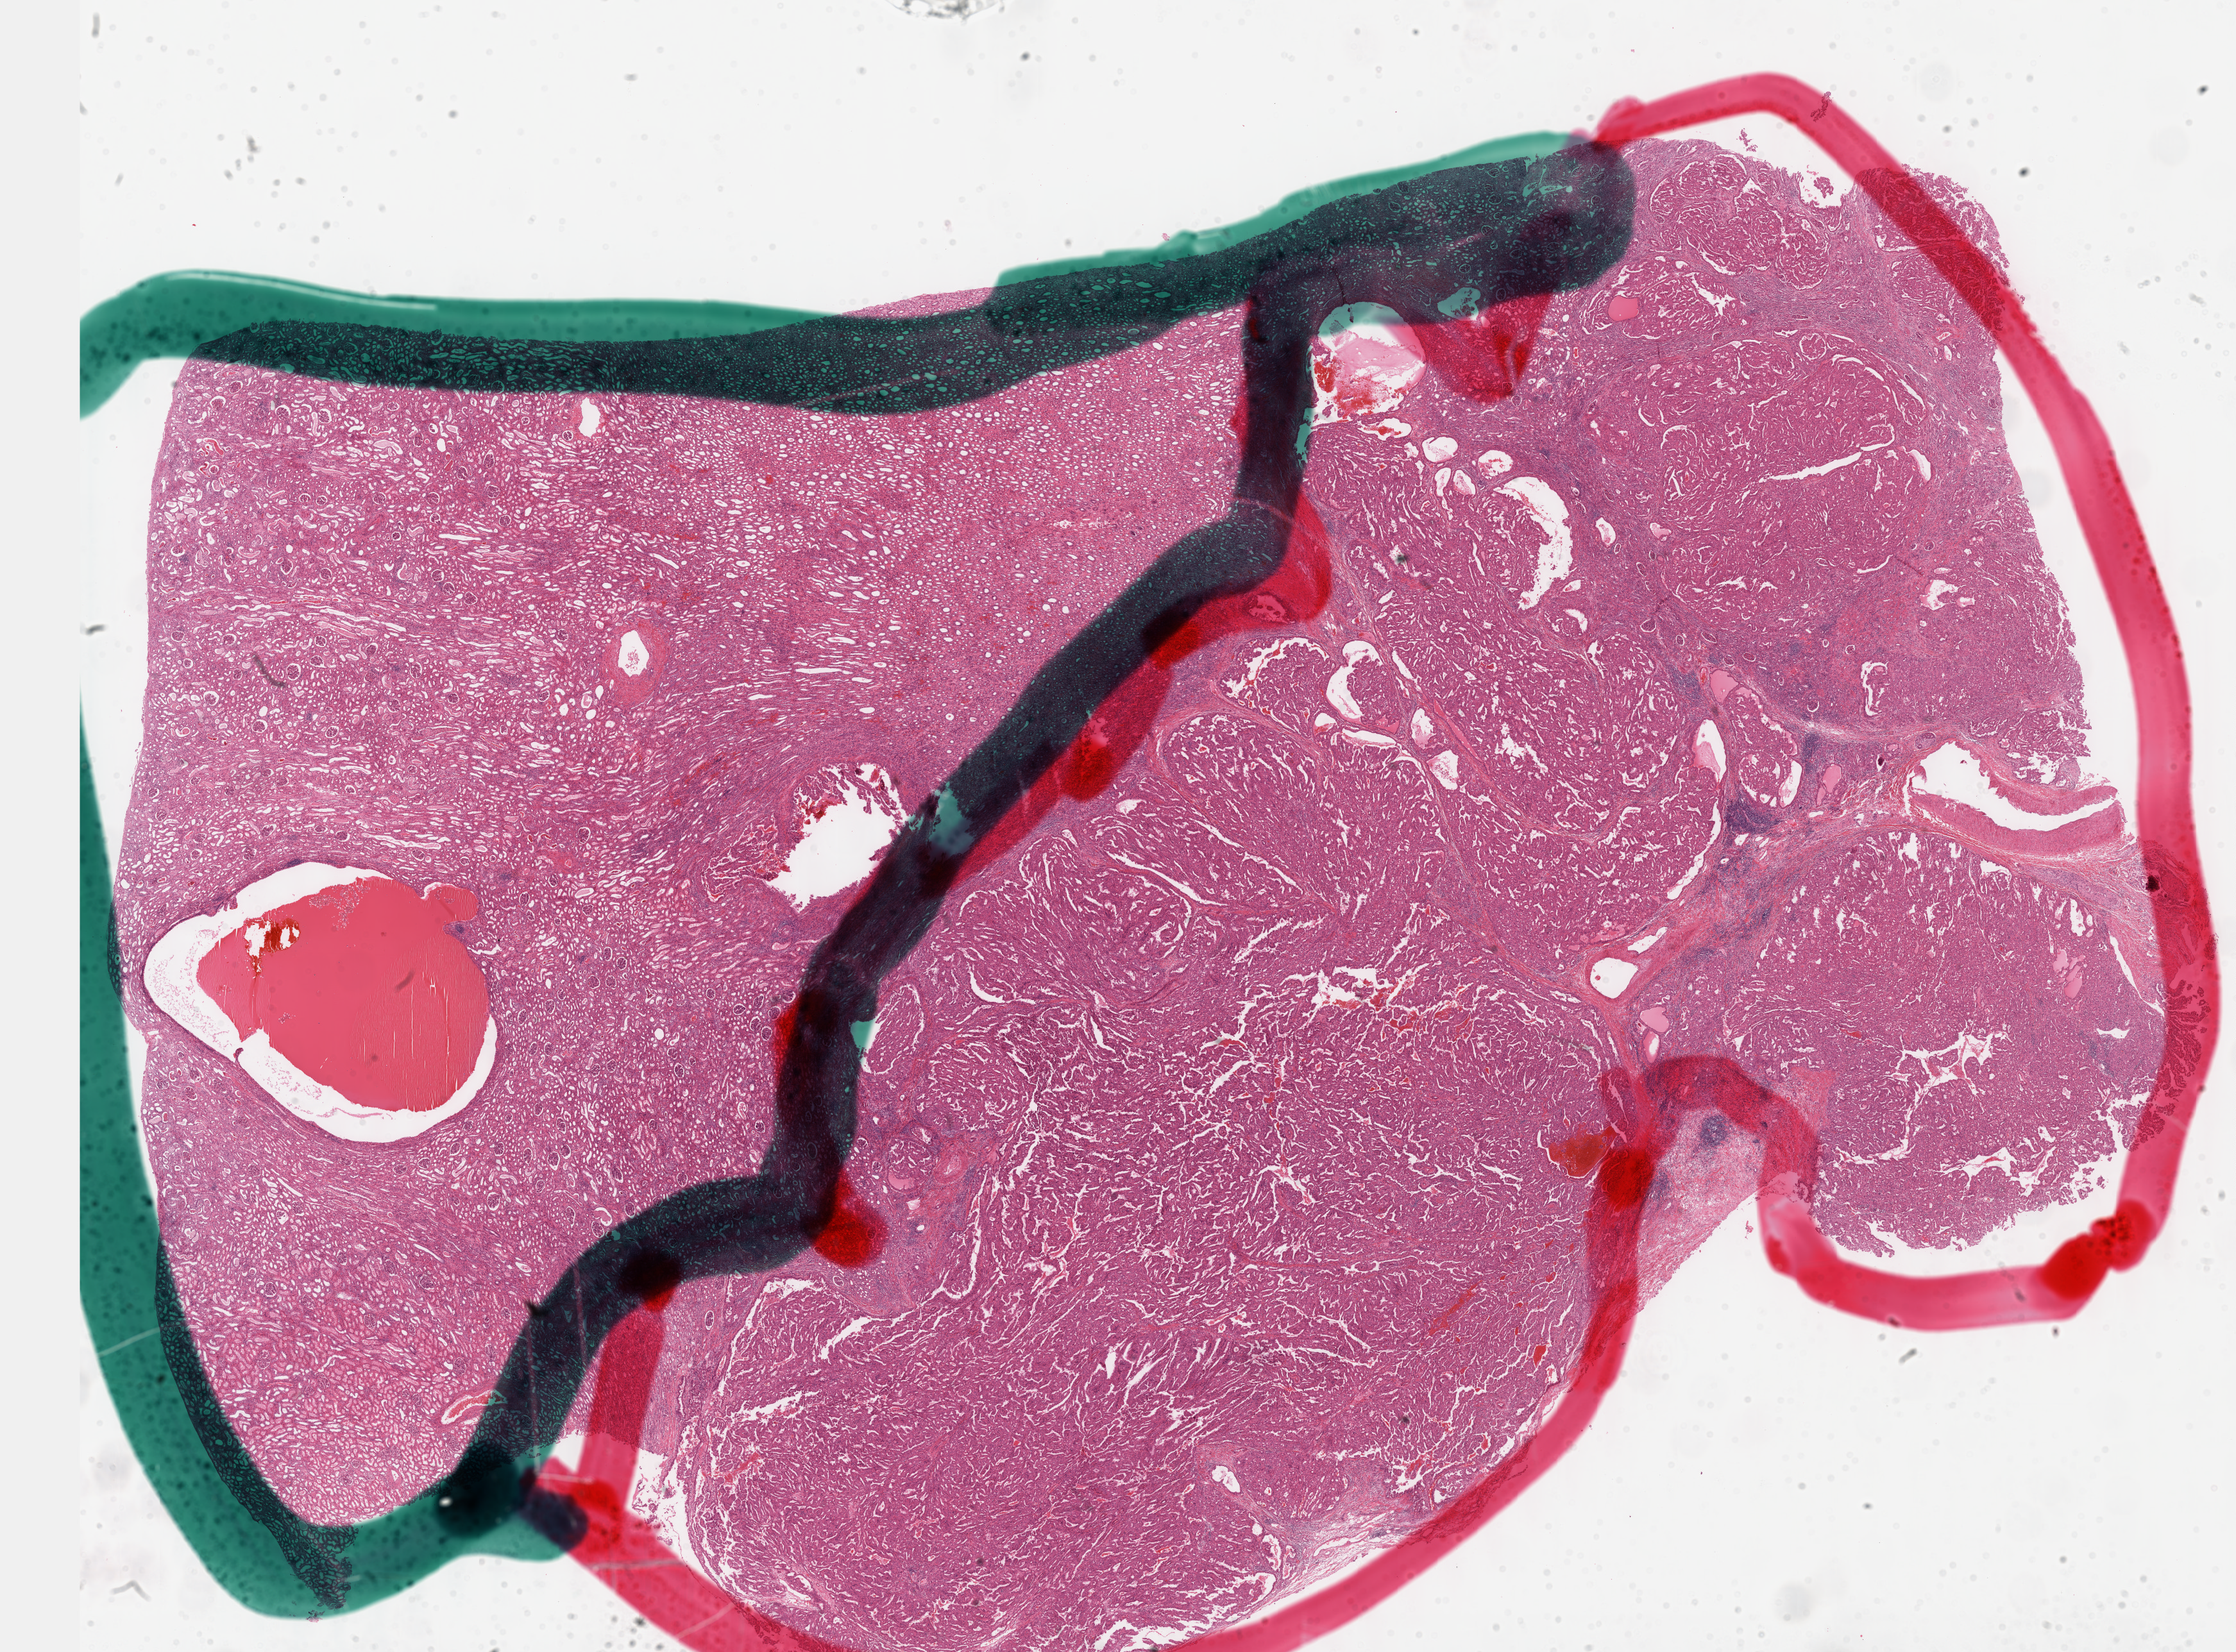
Whole-slide histology image, H&E-stained, whole scanned area (about 28.2 x 20.8 mm) shown as a low-resolution overview. FFPE section. Primary tumour sample from the kidney. Female, age 38 years at initial diagnosis.
Histologic diagnosis: Papillary adenocarcinoma, NOS.